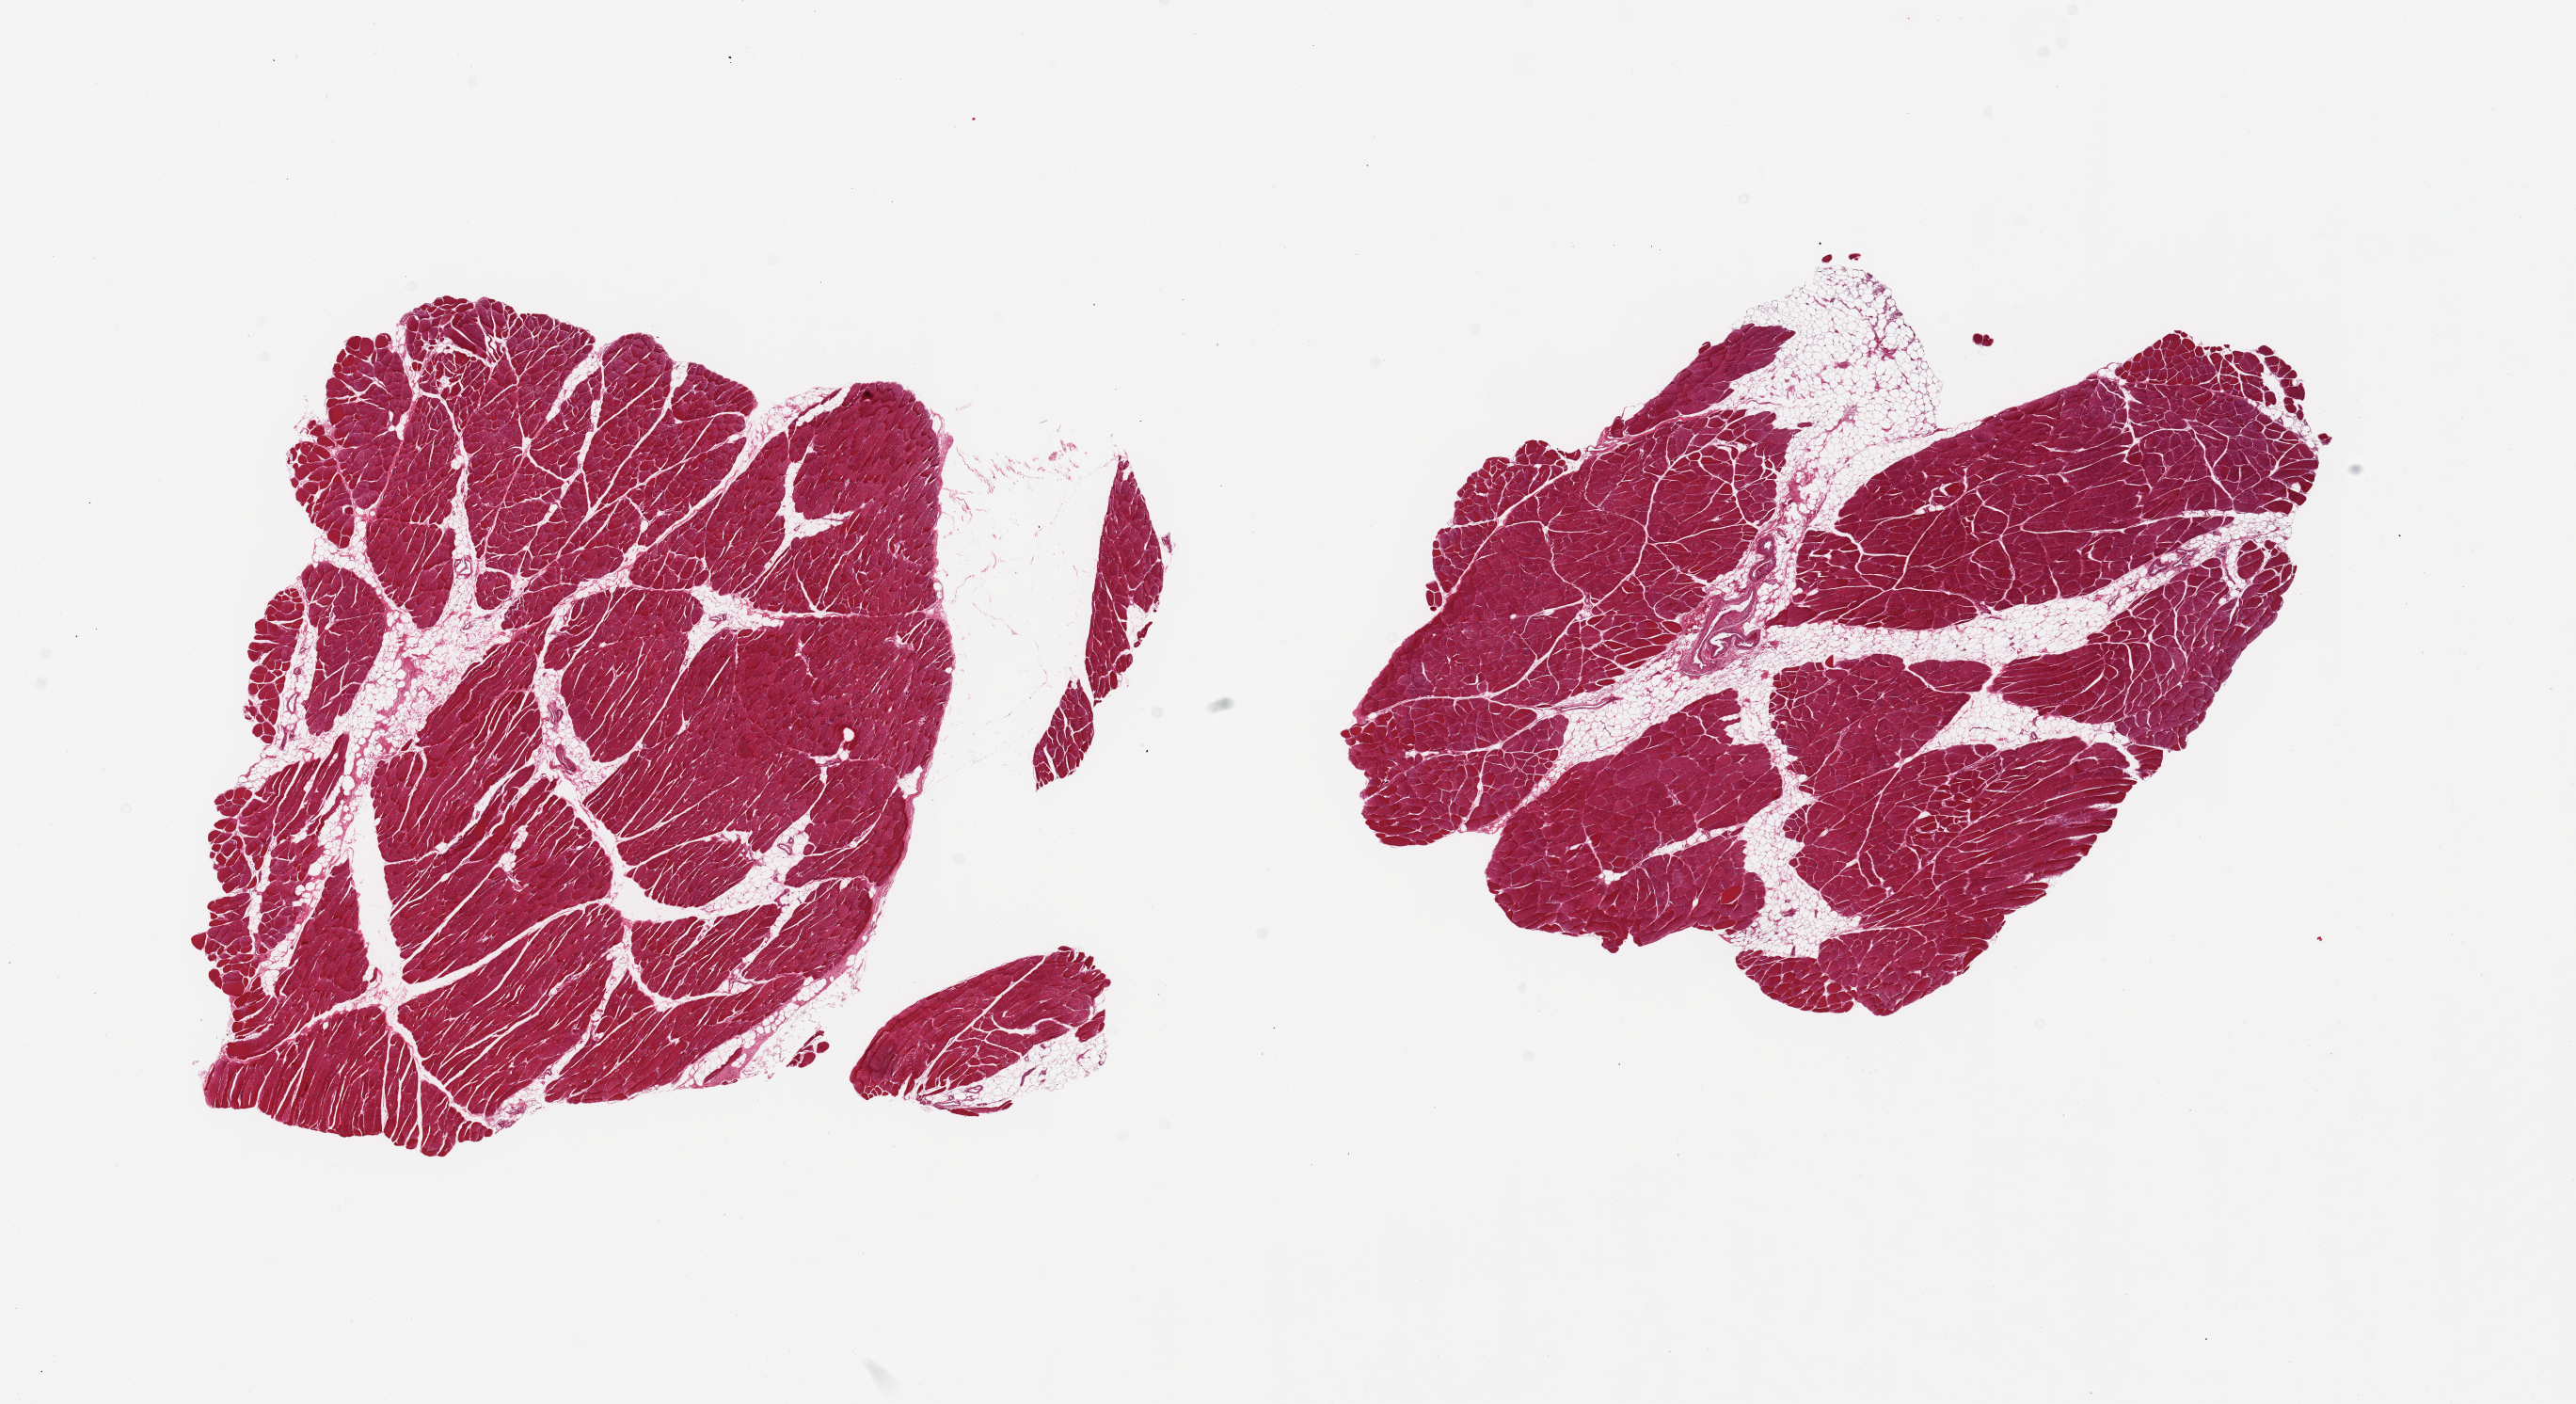
H&E whole-slide image, brightfield — low-resolution overview of the scanned area, about 21.7 x 11.8 mm; PAXgene-fixed, paraffin-embedded tissue; target tissue: skeletal muscle; donor tissue sample. Donor sex: male.
Review note (as recorded): 2 pieces, ~10-20% interstitial fat/vascular elements.